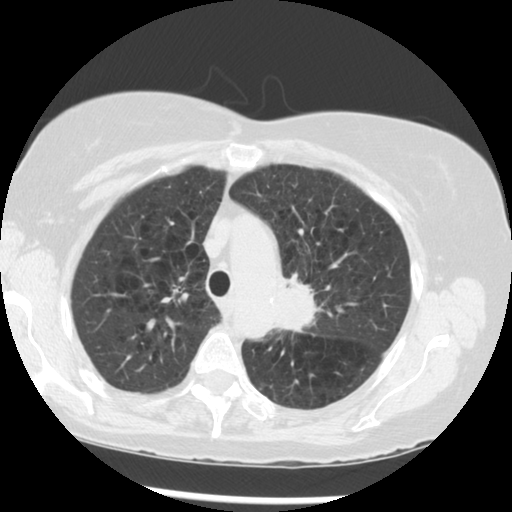
Axial slice from a low-dose chest CT screening exam. Third annual screen. Lung window (W 1500 / L -600 HU). Slice 213 of 283 in the series. Female, age 70 years at enrolment. Current smoker at enrolment.
Expert-annotated lung lesion, bounding box (x1, y1, x2, y2) in pixels: (267, 266, 361, 356). The exam's reader record, not a measurement of the box and not confirmed to be the same lesion: non-calcified nodule or mass ≥4 mm, left upper lobe, 32 × 26 mm, spiculated (stellate) margins, soft tissue attenuation, pre-existing on the prior screen: yes; interval growth: yes. Lung cancer was diagnosed 24 days after this screen: neoplasm, malignant, left upper lobe, stage IIIB (AJCC 6th edition), 40 mm at pathology.